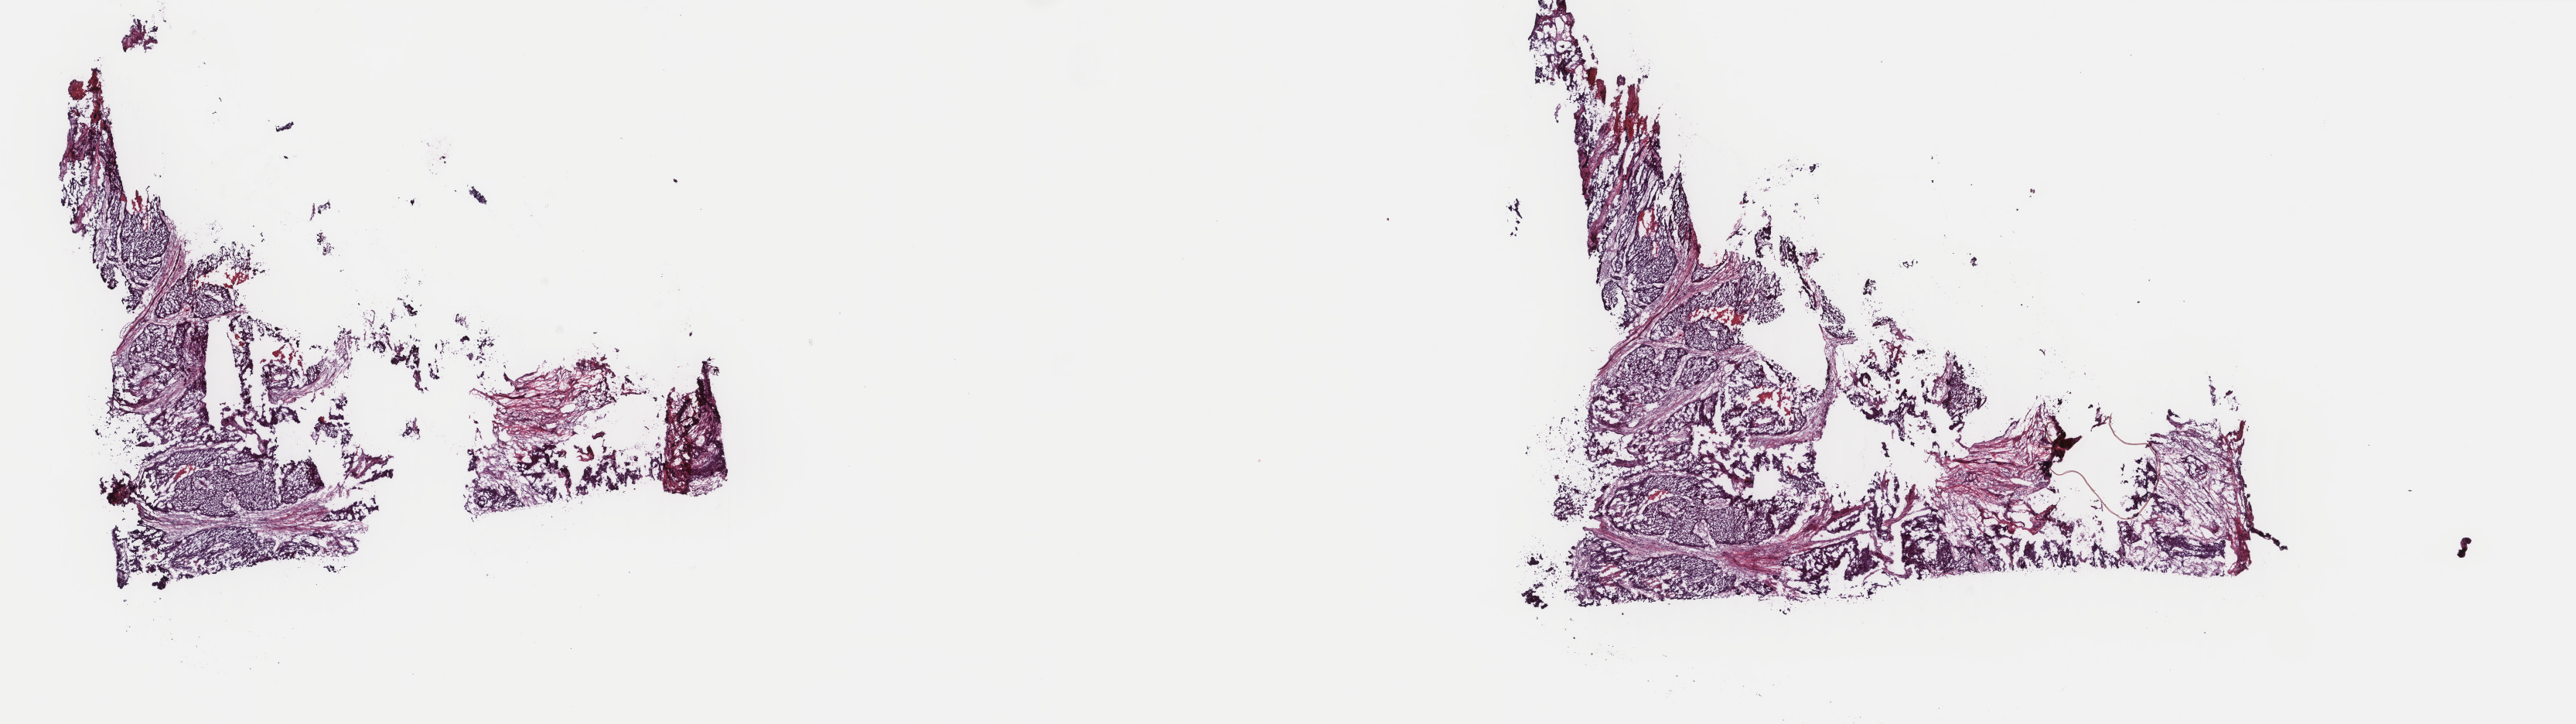
Whole-slide histology image, H&E — a low-resolution overview of the entire scanned area, about 26.4 x 7.4 mm (slide scanned at 40x); frozen section; primary tumour sample from the head and neck. Patient: female, age at initial diagnosis 69 years. Histologic grade: G2 (moderately differentiated). Pathologist review of this section (percent, as recorded): tumour cells 75%, tumour nuclei 80%, normal cells 0%, stromal cells 25%, necrosis 0%. Inflammatory infiltration, as recorded: lymphocyte infiltration 0%, monocyte infiltration 0%, neutrophil infiltration 0%.
* lymph nodes positive (case pathology): 1 of 7 examined
* histologic diagnosis: Basaloid squamous cell carcinoma (larynx, NOS)
* AJCC pathologic stage: III
* TNM: T1 N1 MX
* laterality: midline